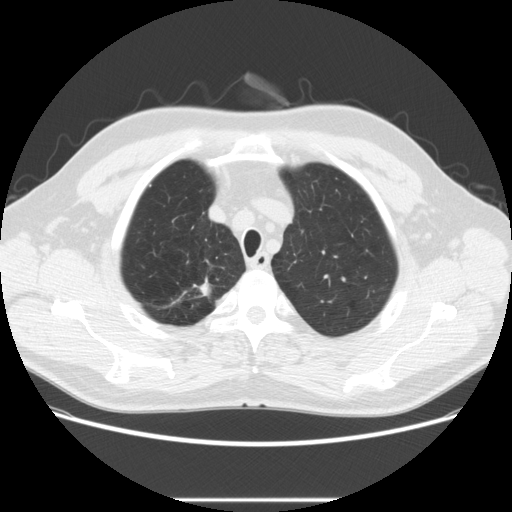
Low-dose screening chest CT, axial slice. Baseline annual screen. Lung window (W 1500 / L -600 HU). 2.5 mm slice thickness. Slice 39 of 270 in the series. 512 × 512 image matrix. Male, age 64 years at enrolment. Former smoker at enrolment.
Lesion marked by an expert reader, bounding box [x1, y1, x2, y2] px = [174, 279, 220, 308]. The screening reader recorded 2 non-calcified nodules or masses ≥4 mm on this exam (right upper lobe, right upper lobe); which of them this box marks is not recorded. Official screen result: positive, change unspecified: nodule(s) >= 4 mm or enlarging nodule(s), mass(es), or other non-specific abnormalities suspicious for lung cancer. Lung cancer was diagnosed 753 days after this screen (after the third annual screen): adenocarcinoma, NOS, right upper lobe, moderately differentiated (G2), stage IA (AJCC 6th edition), 14 mm at pathology.